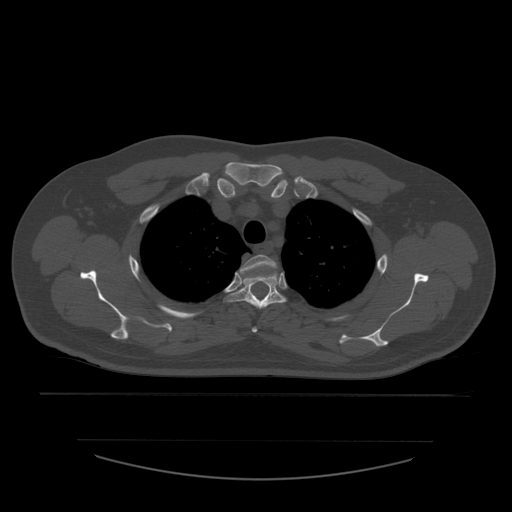
CT including the spine, one axial slice; position 438 of 532 along the scan axis; bone window (W 1800 / L 400 HU); 512 × 512 image matrix. Patient age 44 years. From the clinical record (not read from this slice): primary cancer: soft tissue sarcoma.
Annotated regions visible in this slice (semi-automatically segmented with operator editing):
- T2 vertebra: bounding box [x1, y1, x2, y2] px = [240, 255, 277, 333]
- T3 vertebra: [228, 272, 287, 309]